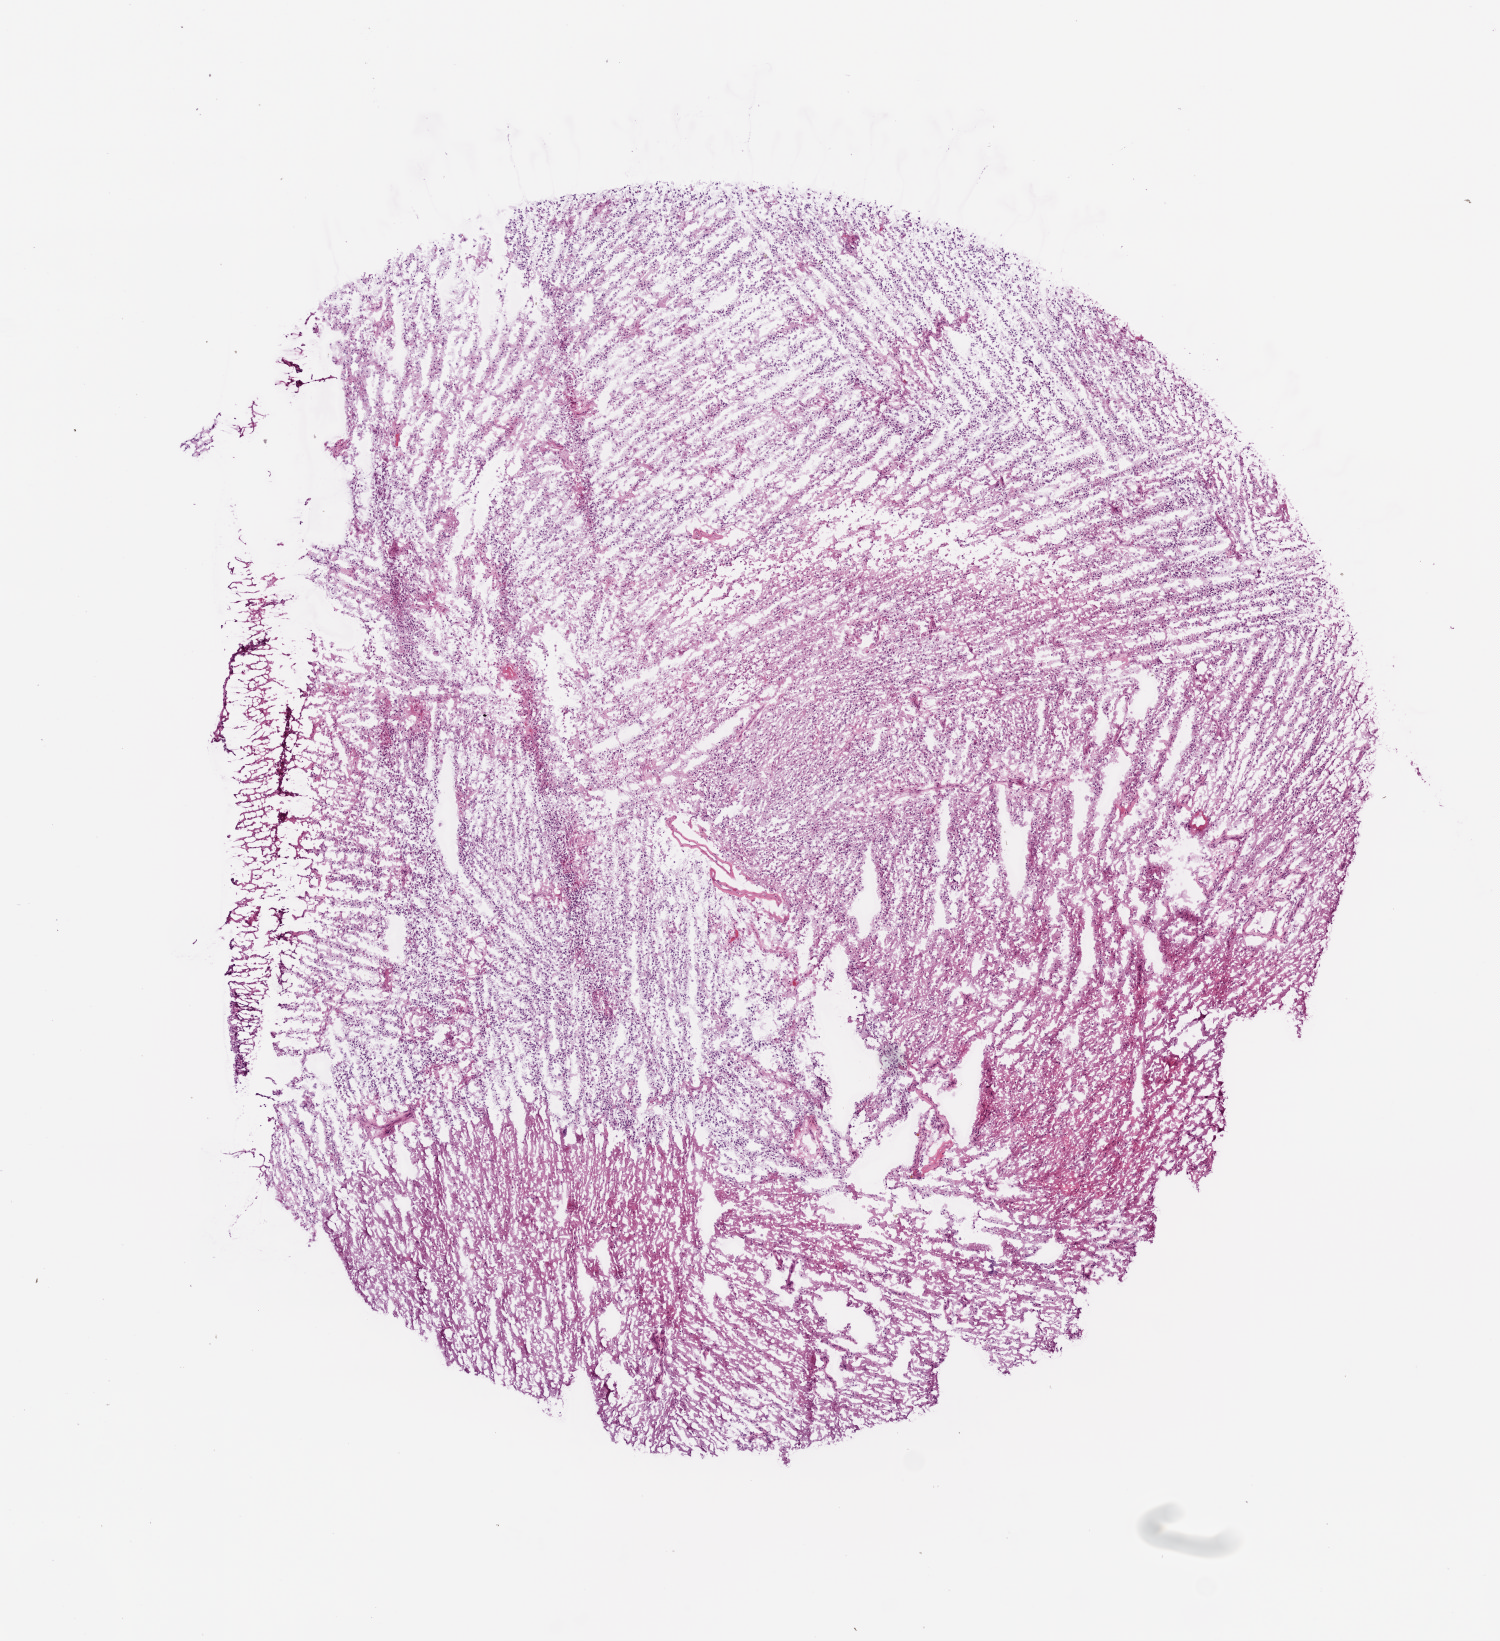
Whole-slide histology image, H&E — a low-resolution overview of the entire scanned area, about 6.0 x 6.6 mm (acquisition: 20x scan), frozen section, brain, primary tumour sample. Patient: male, age at initial diagnosis 74 years. Composition of this section per pathologist review: tumour cells 95%, tumour nuclei 80%, normal cells 0%, stromal cells 0%, necrosis 5%.
Histologic diagnosis: Glioblastoma.